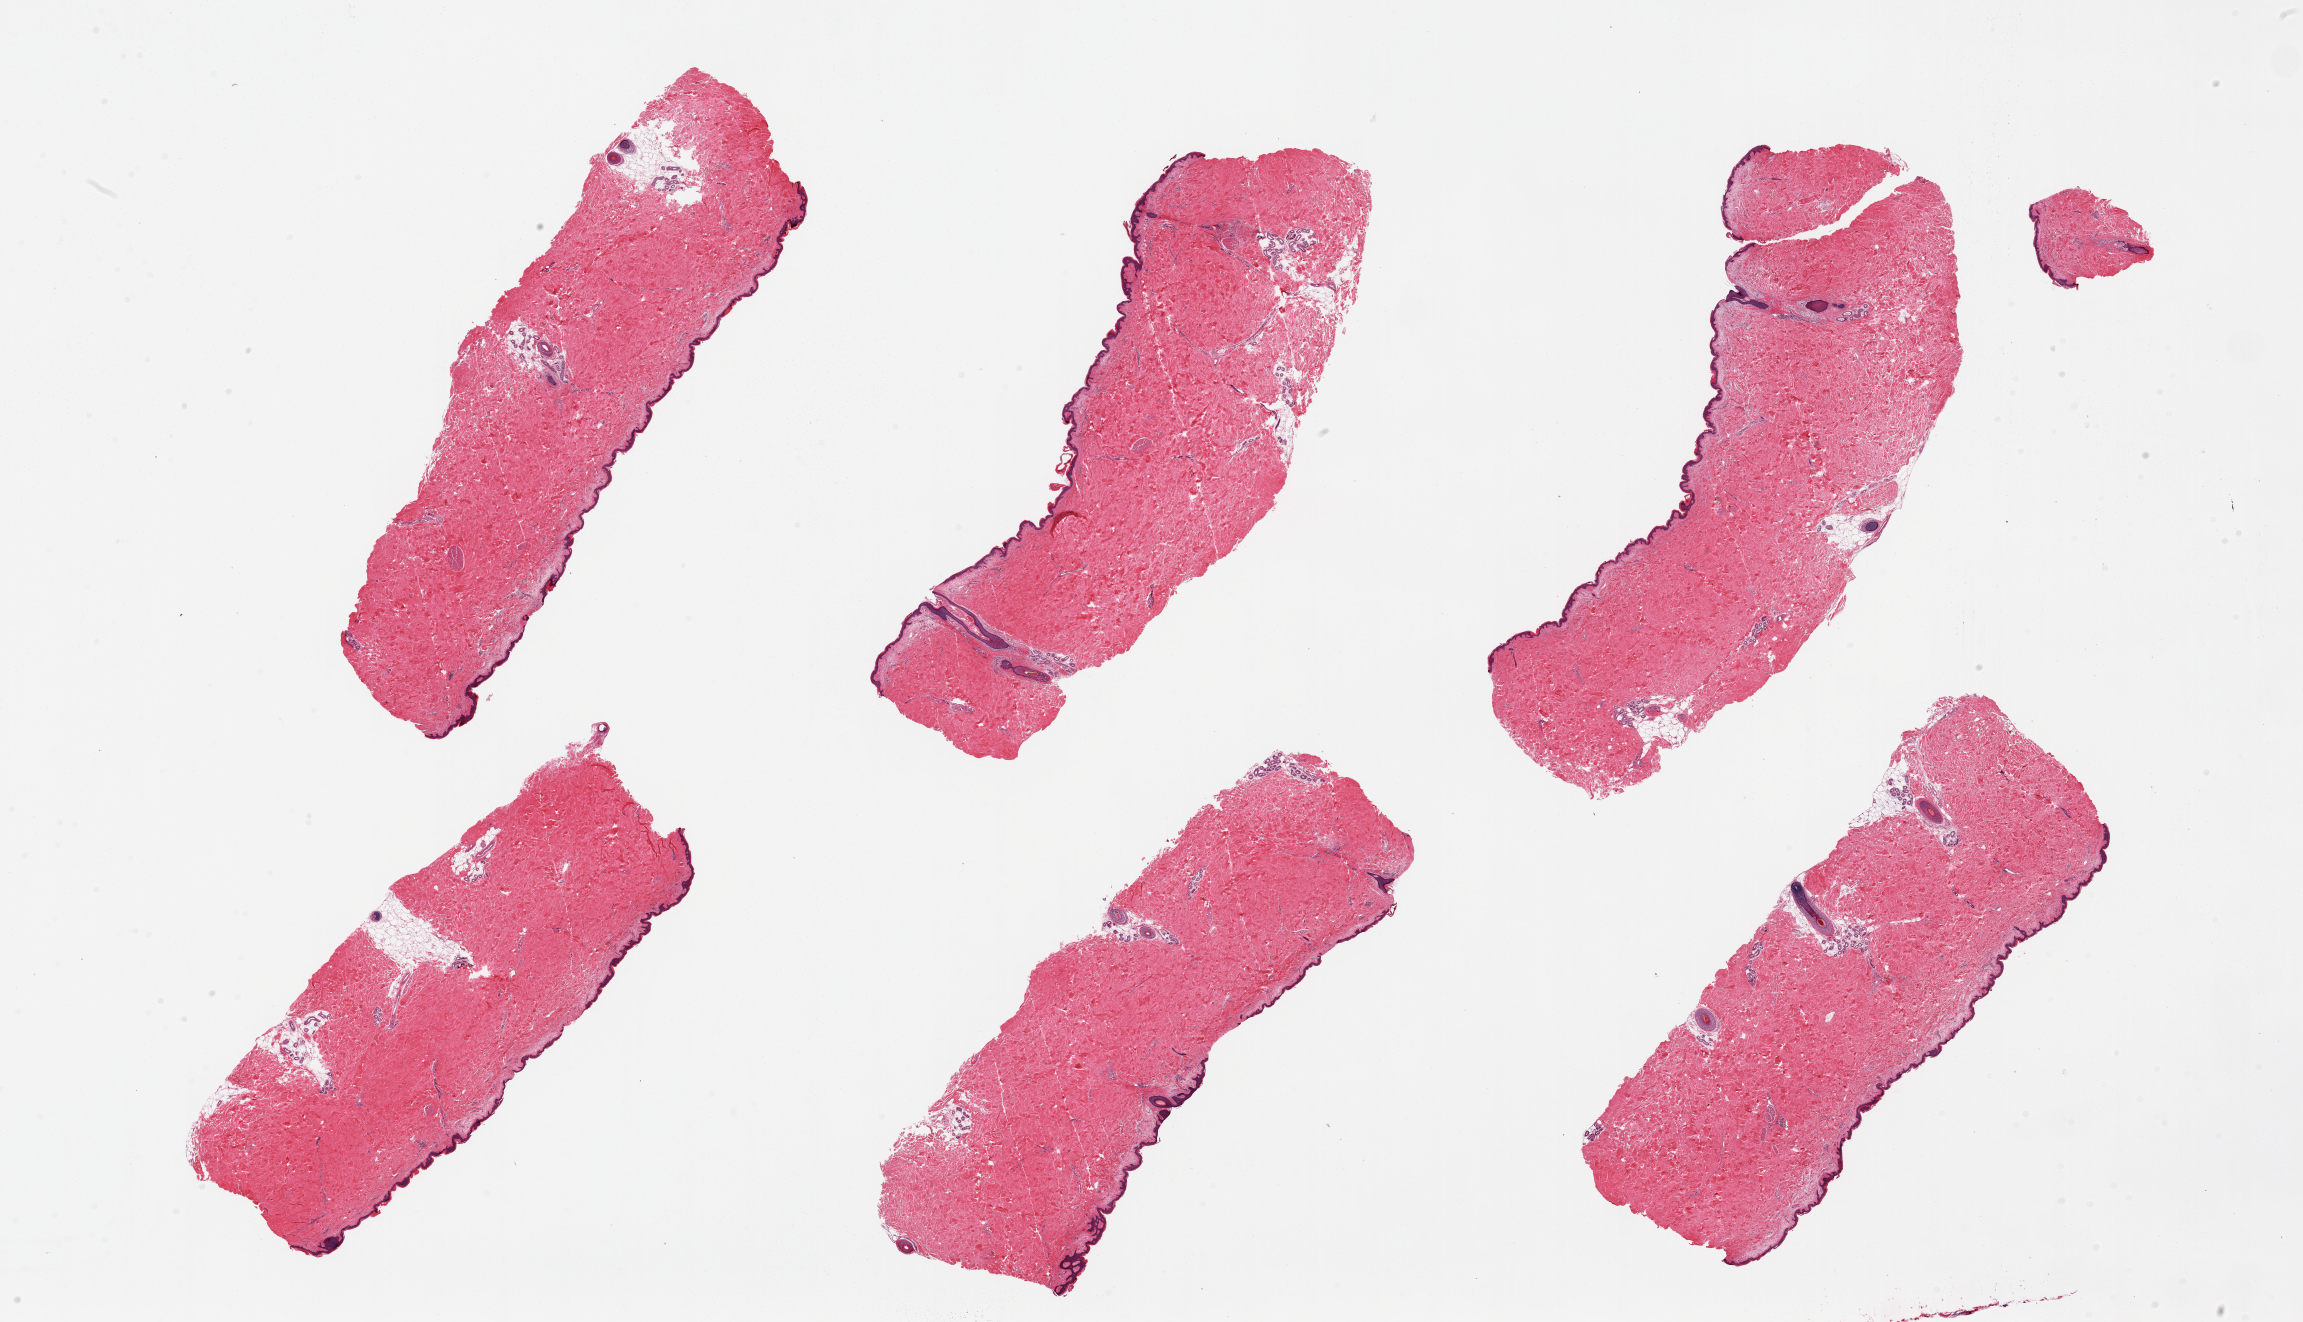
Whole-slide image, haematoxylin and eosin stain, brightfield — low-resolution overview of the scanned area, about 36.4 x 20.9 mm (acquisition: 20x scan). PAXgene-fixed paraffin-embedded (PFPE) section. Target tissue: skin of suprapubic region. Donor tissue sample.
Reviewer comment on this tissue sample: 6 pieces, from 8.6x3 to 11x3mm; well trimmed.